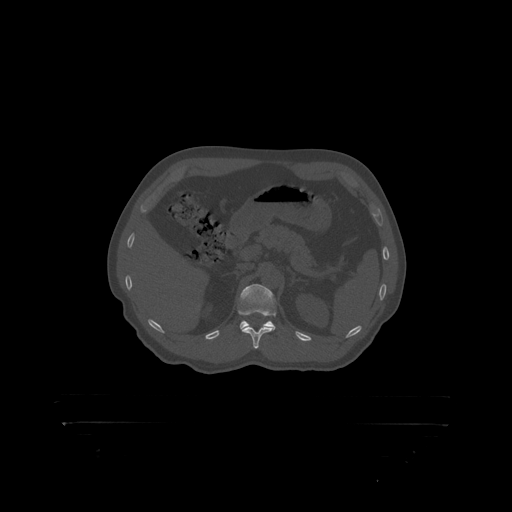
CT including the spine, one axial slice; position 340 of 399 along the scan axis; reconstruction kernel STANDARD; 120 kVp; bone window (W 1800 / L 400 HU); 1.25 mm slice thickness; 512 × 512 image matrix. Patient: male, 46 years. Case-level facts recorded for this patient, not image findings: primary cancer: skin.
Annotated regions visible in this slice (semi-automatically segmented with operator editing):
- L1 vertebra: bounding box (x1, y1, x2, y2) in pixels: (239, 285, 276, 317)